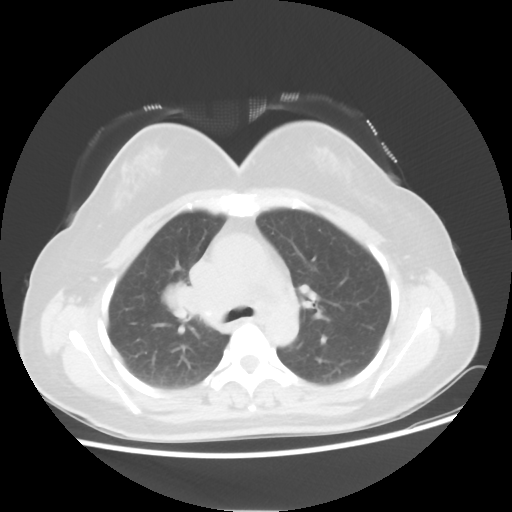
Chest CT, one axial slice; position 34 of 50 along the scan axis; reconstruction kernel STANDARD; lung window (W 1500 / L -600 HU); 5 mm slice thickness; 512 × 512 image matrix. Female patient, age 40 years. Case-level facts recorded for this patient, not image findings: clinical TNM (as recorded): T1c N3 M0; histopathological grade: G3.
Annotated regions visible in this slice (rectangle marked by the reading radiologist):
- lung tumour (recorded histology: small cell carcinoma): box from (x=157, y=281) to (x=195, y=330) px